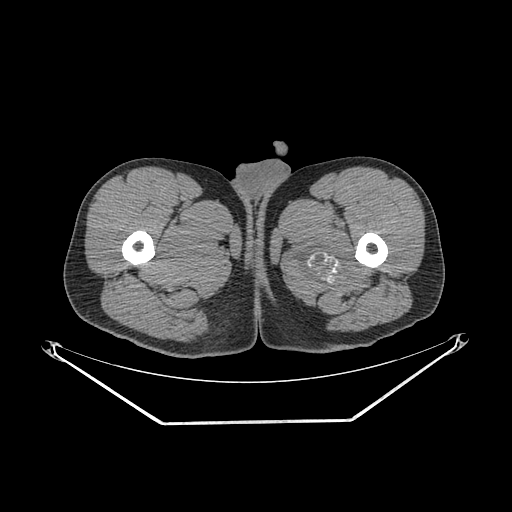
CT of an extremity soft-tissue mass (from a PET/CT study), one axial slice. Position 259 of 267 along the scan axis. 140 kVp. Soft-tissue window (W 400 / L 40 HU). 3.75 mm slice thickness. 512 × 512 image matrix, field of view 500 × 500 mm. Male patient. From the clinical record (not read from this slice): histological type: extraskeletal osteosarcoma; grade: high; site of the primary tumour: left adductur.
Annotated regions visible in this slice (expert contour drawn on MRI and transferred to this co-registered scan by the dataset authors):
- gross tumour volume (mass): bounding box [x1, y1, x2, y2] px = [288, 210, 380, 300]